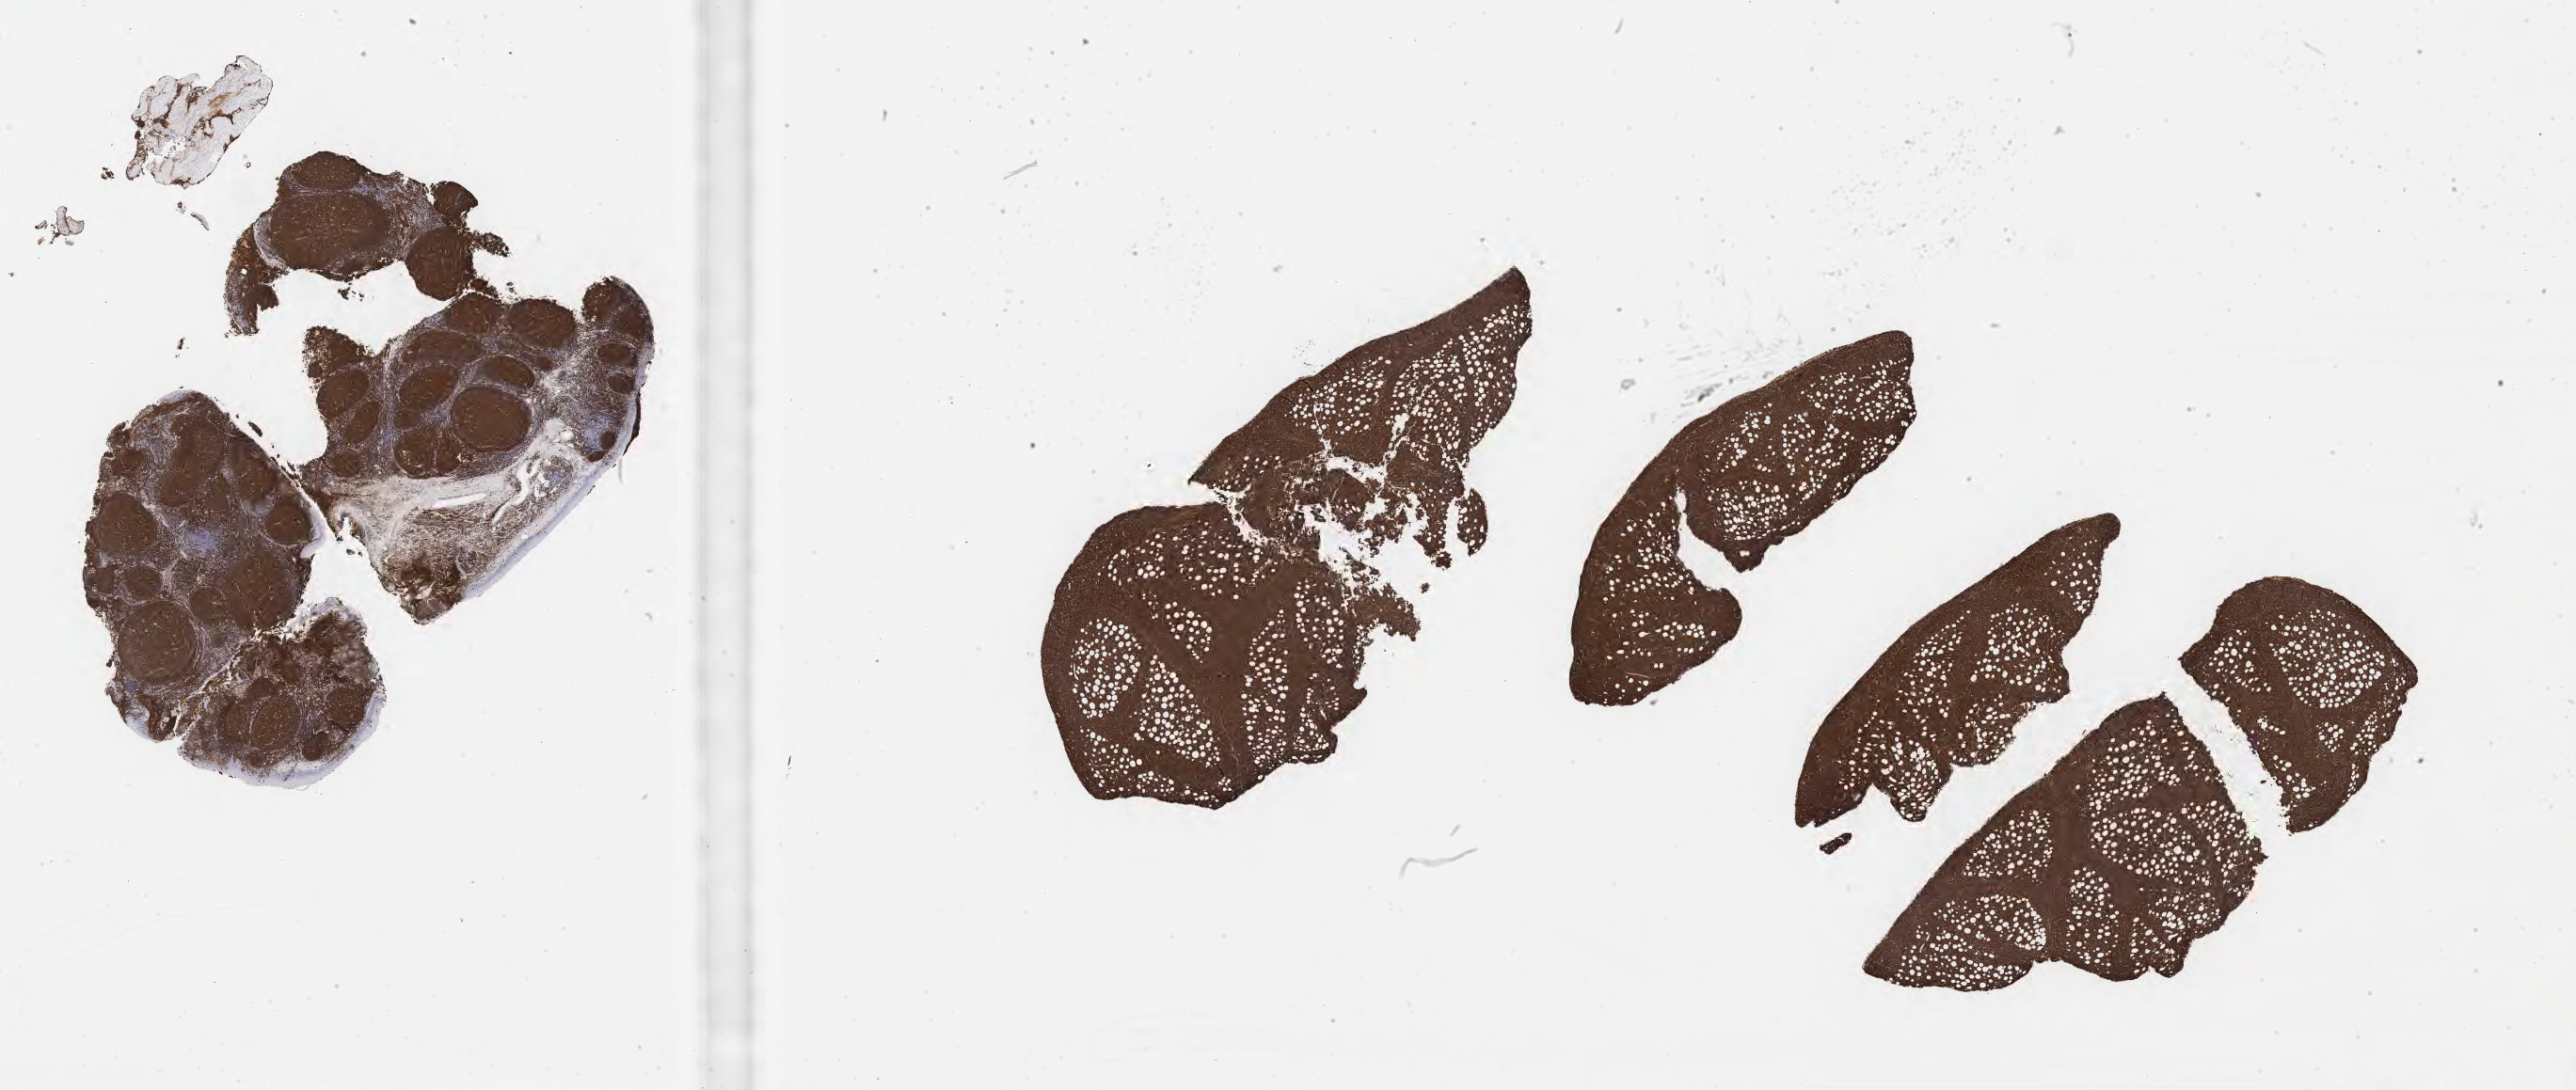
Whole-slide image, immunohistochemical stain for CD20 — low-resolution overview of the scanned area, about 44.3 x 18.8 mm; tumor tissue. Male patient, age 52 years.
Diagnosis: Diffuse large B-cell lymphoma, NOS.